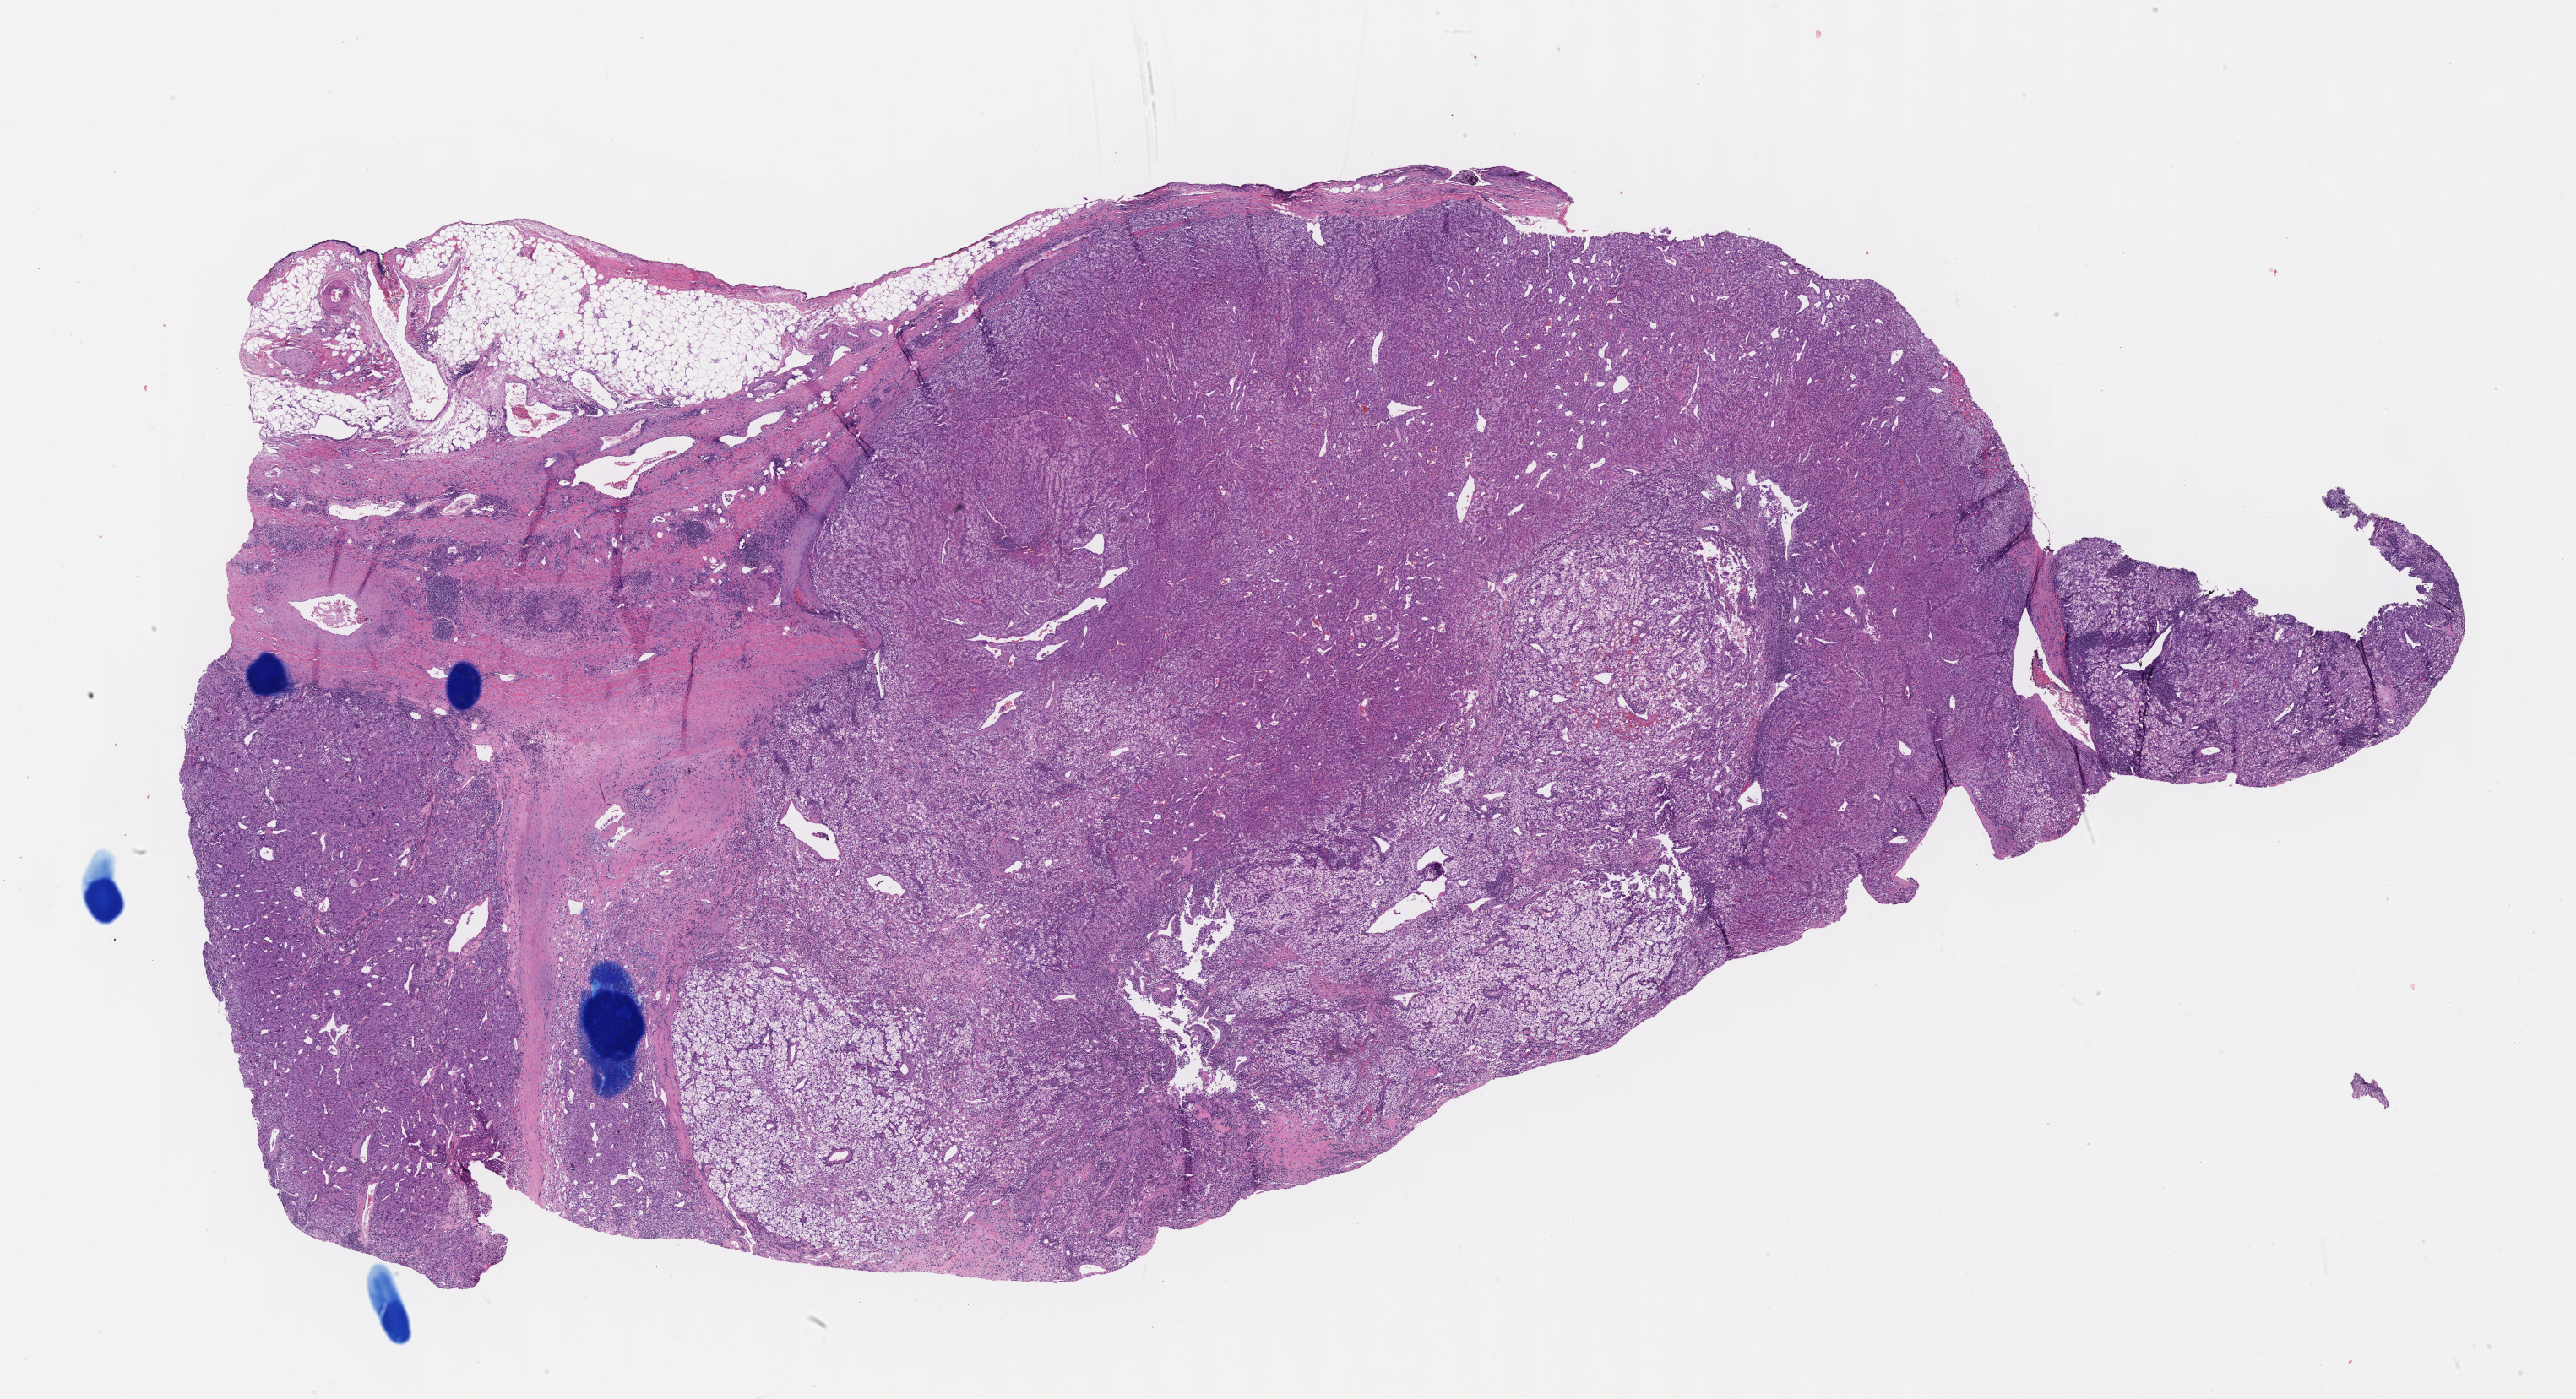
Digitized Hematoxylin and eosin (H&E) stained tissue section (whole slide) — low-resolution overview of the scanned area, about 24.7 x 13.4 mm (slide scanned at 40x). Formalin-fixed paraffin-embedded (FFPE) diagnostic section. Kidney, primary tumour sample. Patient: female, age at initial diagnosis 69 years. Histologic grade: G4 (undifferentiated).
Lymph nodes positive (case pathology): 1 of 14 examined. AJCC pathologic stage: IV. Diagnosis: Clear cell adenocarcinoma, NOS.